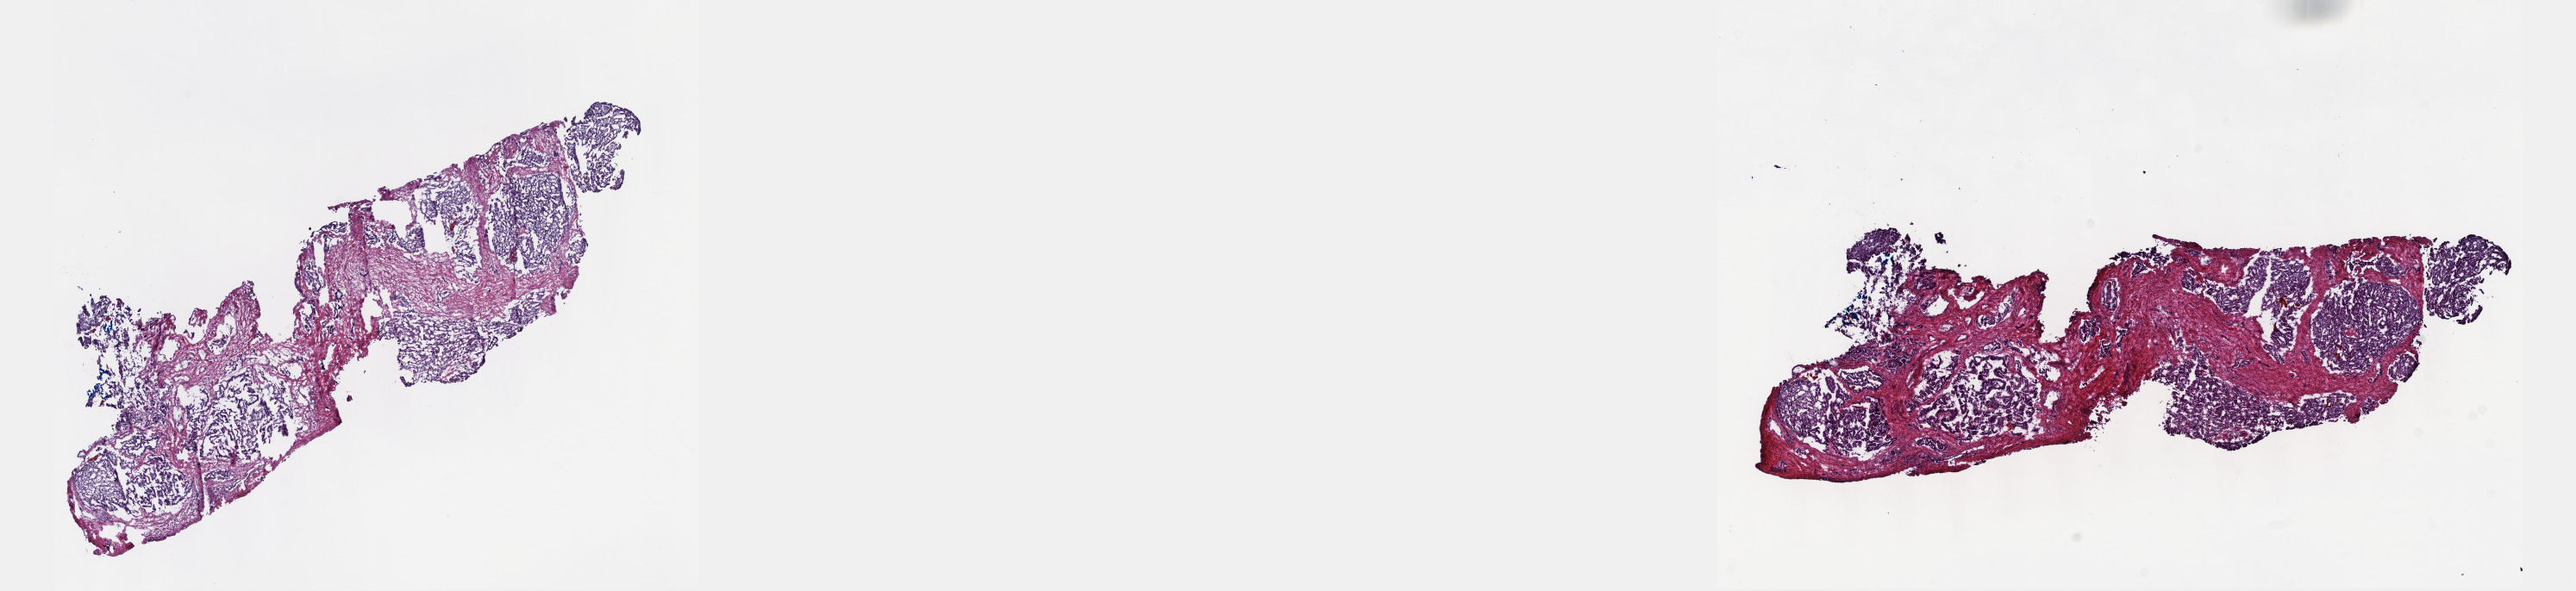
Whole-slide histology image, H&E — a low-resolution overview of the entire scanned area, about 24.1 x 5.5 mm. Frozen section. Sample: primary tumour, prostate. Male, age 62 years at initial diagnosis. Slide review estimates, as recorded: tumour cells 60%, tumour nuclei 70%.
Pathologic diagnosis: Adenocarcinoma, NOS.